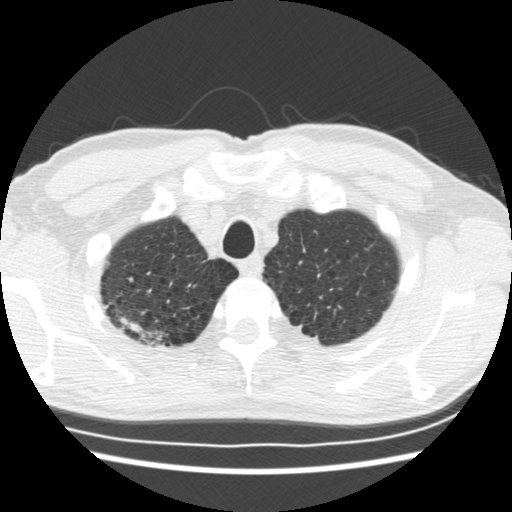
Low-dose screening chest CT, one axial slice; slice 157 of 183 in the series (ordered by position); reconstruction kernel STANDARD; 120 kVp; lung window (W 1500 / L -600 HU); 2.5 mm slice thickness; 512 × 512 image matrix, field of view 339 × 339 mm.
Outlined on this slice (manually delineated by an expert):
- lesion 1 (tumor, upper lobe of right lung): bounding box [x1, y1, x2, y2] px = [119, 316, 163, 343]